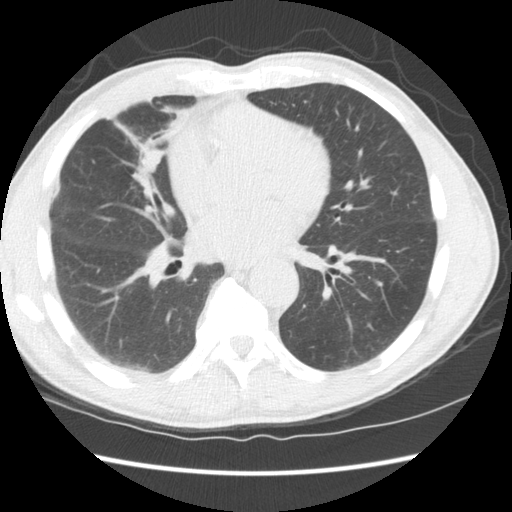
Axial slice from a low-dose chest CT screening exam, third screening round (two years after baseline), lung window (W 1500 / L -600 HU), slice 66 of 147 in the series. Male participant, aged 65 years at enrolment. Current smoker at enrolment.
- Lesion marked by an expert reader, bounding box <104,129,174,209> (left, top, right, bottom; pixels).
- Reader record for this screening exam (exam-level; its link to the box is not recorded): non-calcified nodule or mass ≥4 mm, right middle lobe, 16 × 15 mm, smooth margins, soft tissue attenuation, pre-existing on the prior screen: yes; interval growth: yes.
- Participant outcome: lung cancer diagnosed 357 days after this screen — squamous cell carcinoma, NOS, right middle lobe, poorly differentiated (G3), stage IA (AJCC 6th edition), 23 mm at pathology.